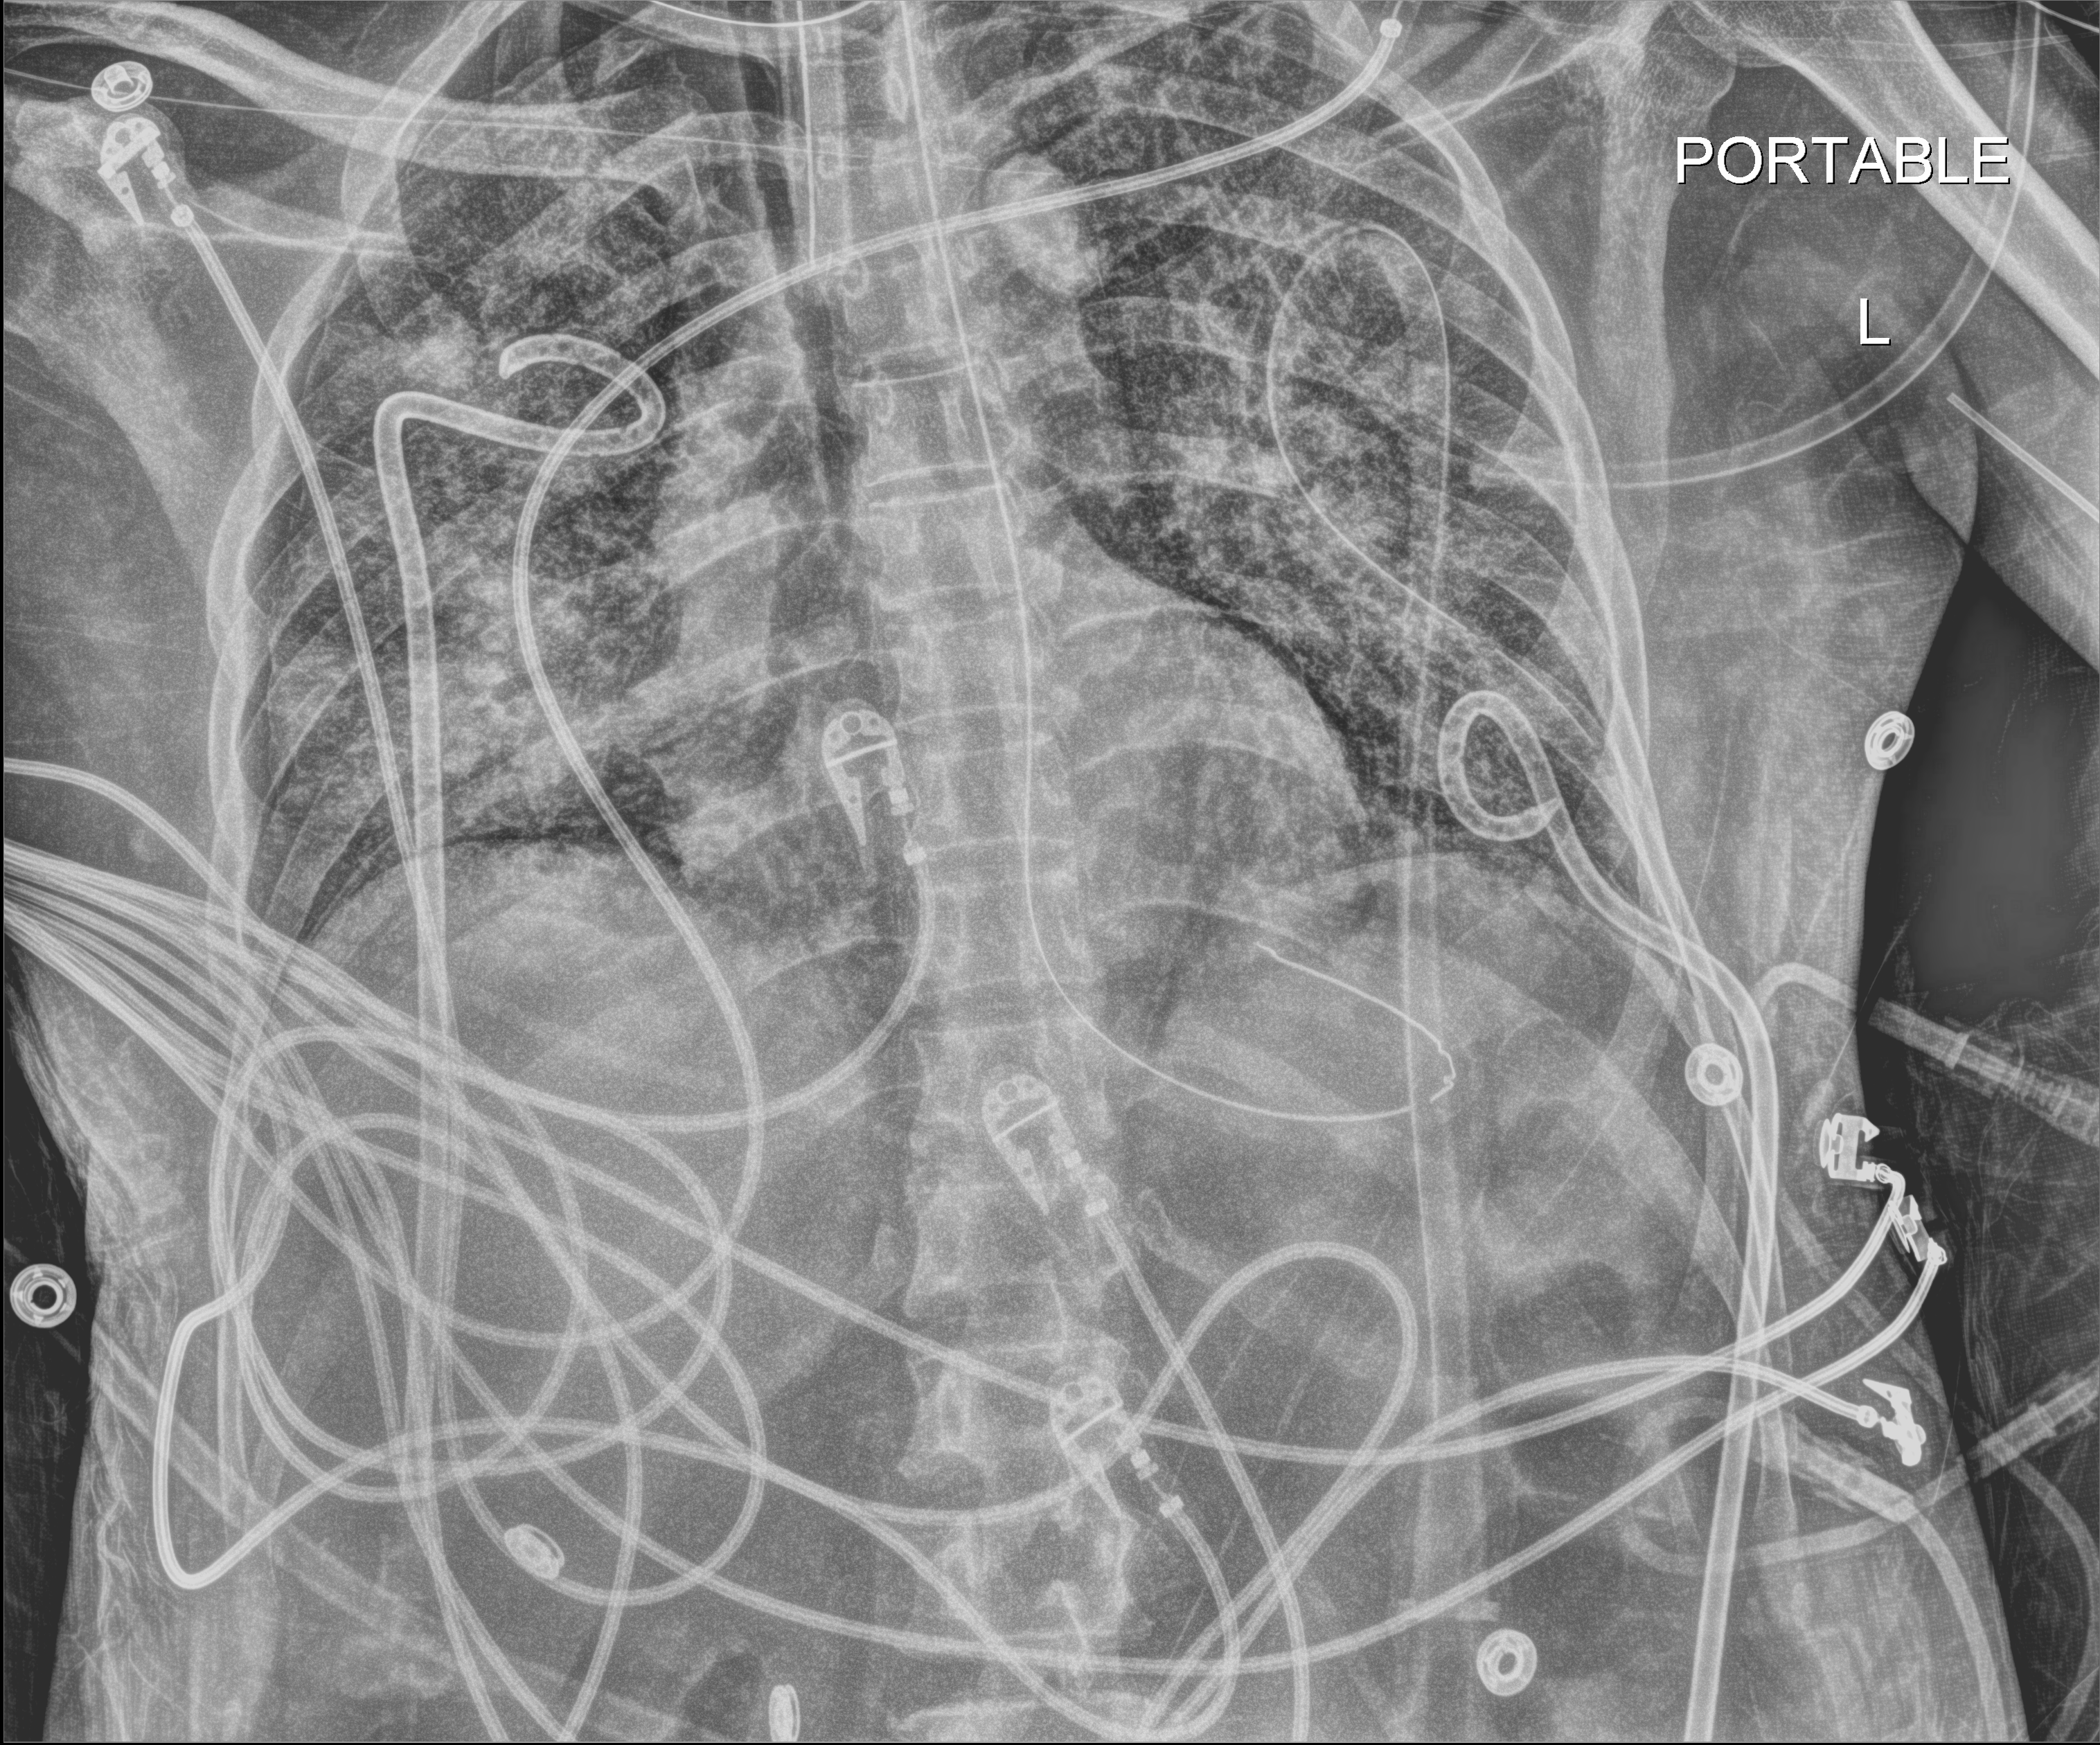
Chest radiograph (digital radiography), anteroposterior (AP) projection. Adult patient hospitalised with COVID-19, age 18–59 years.
Hospital-stay facts (about this admission, not read from this image; timing relative to this image not recorded):
- admitted to intensive care during this hospital stay: yes
- length of hospital stay: 41 days
- mechanically ventilated during this hospital stay: yes